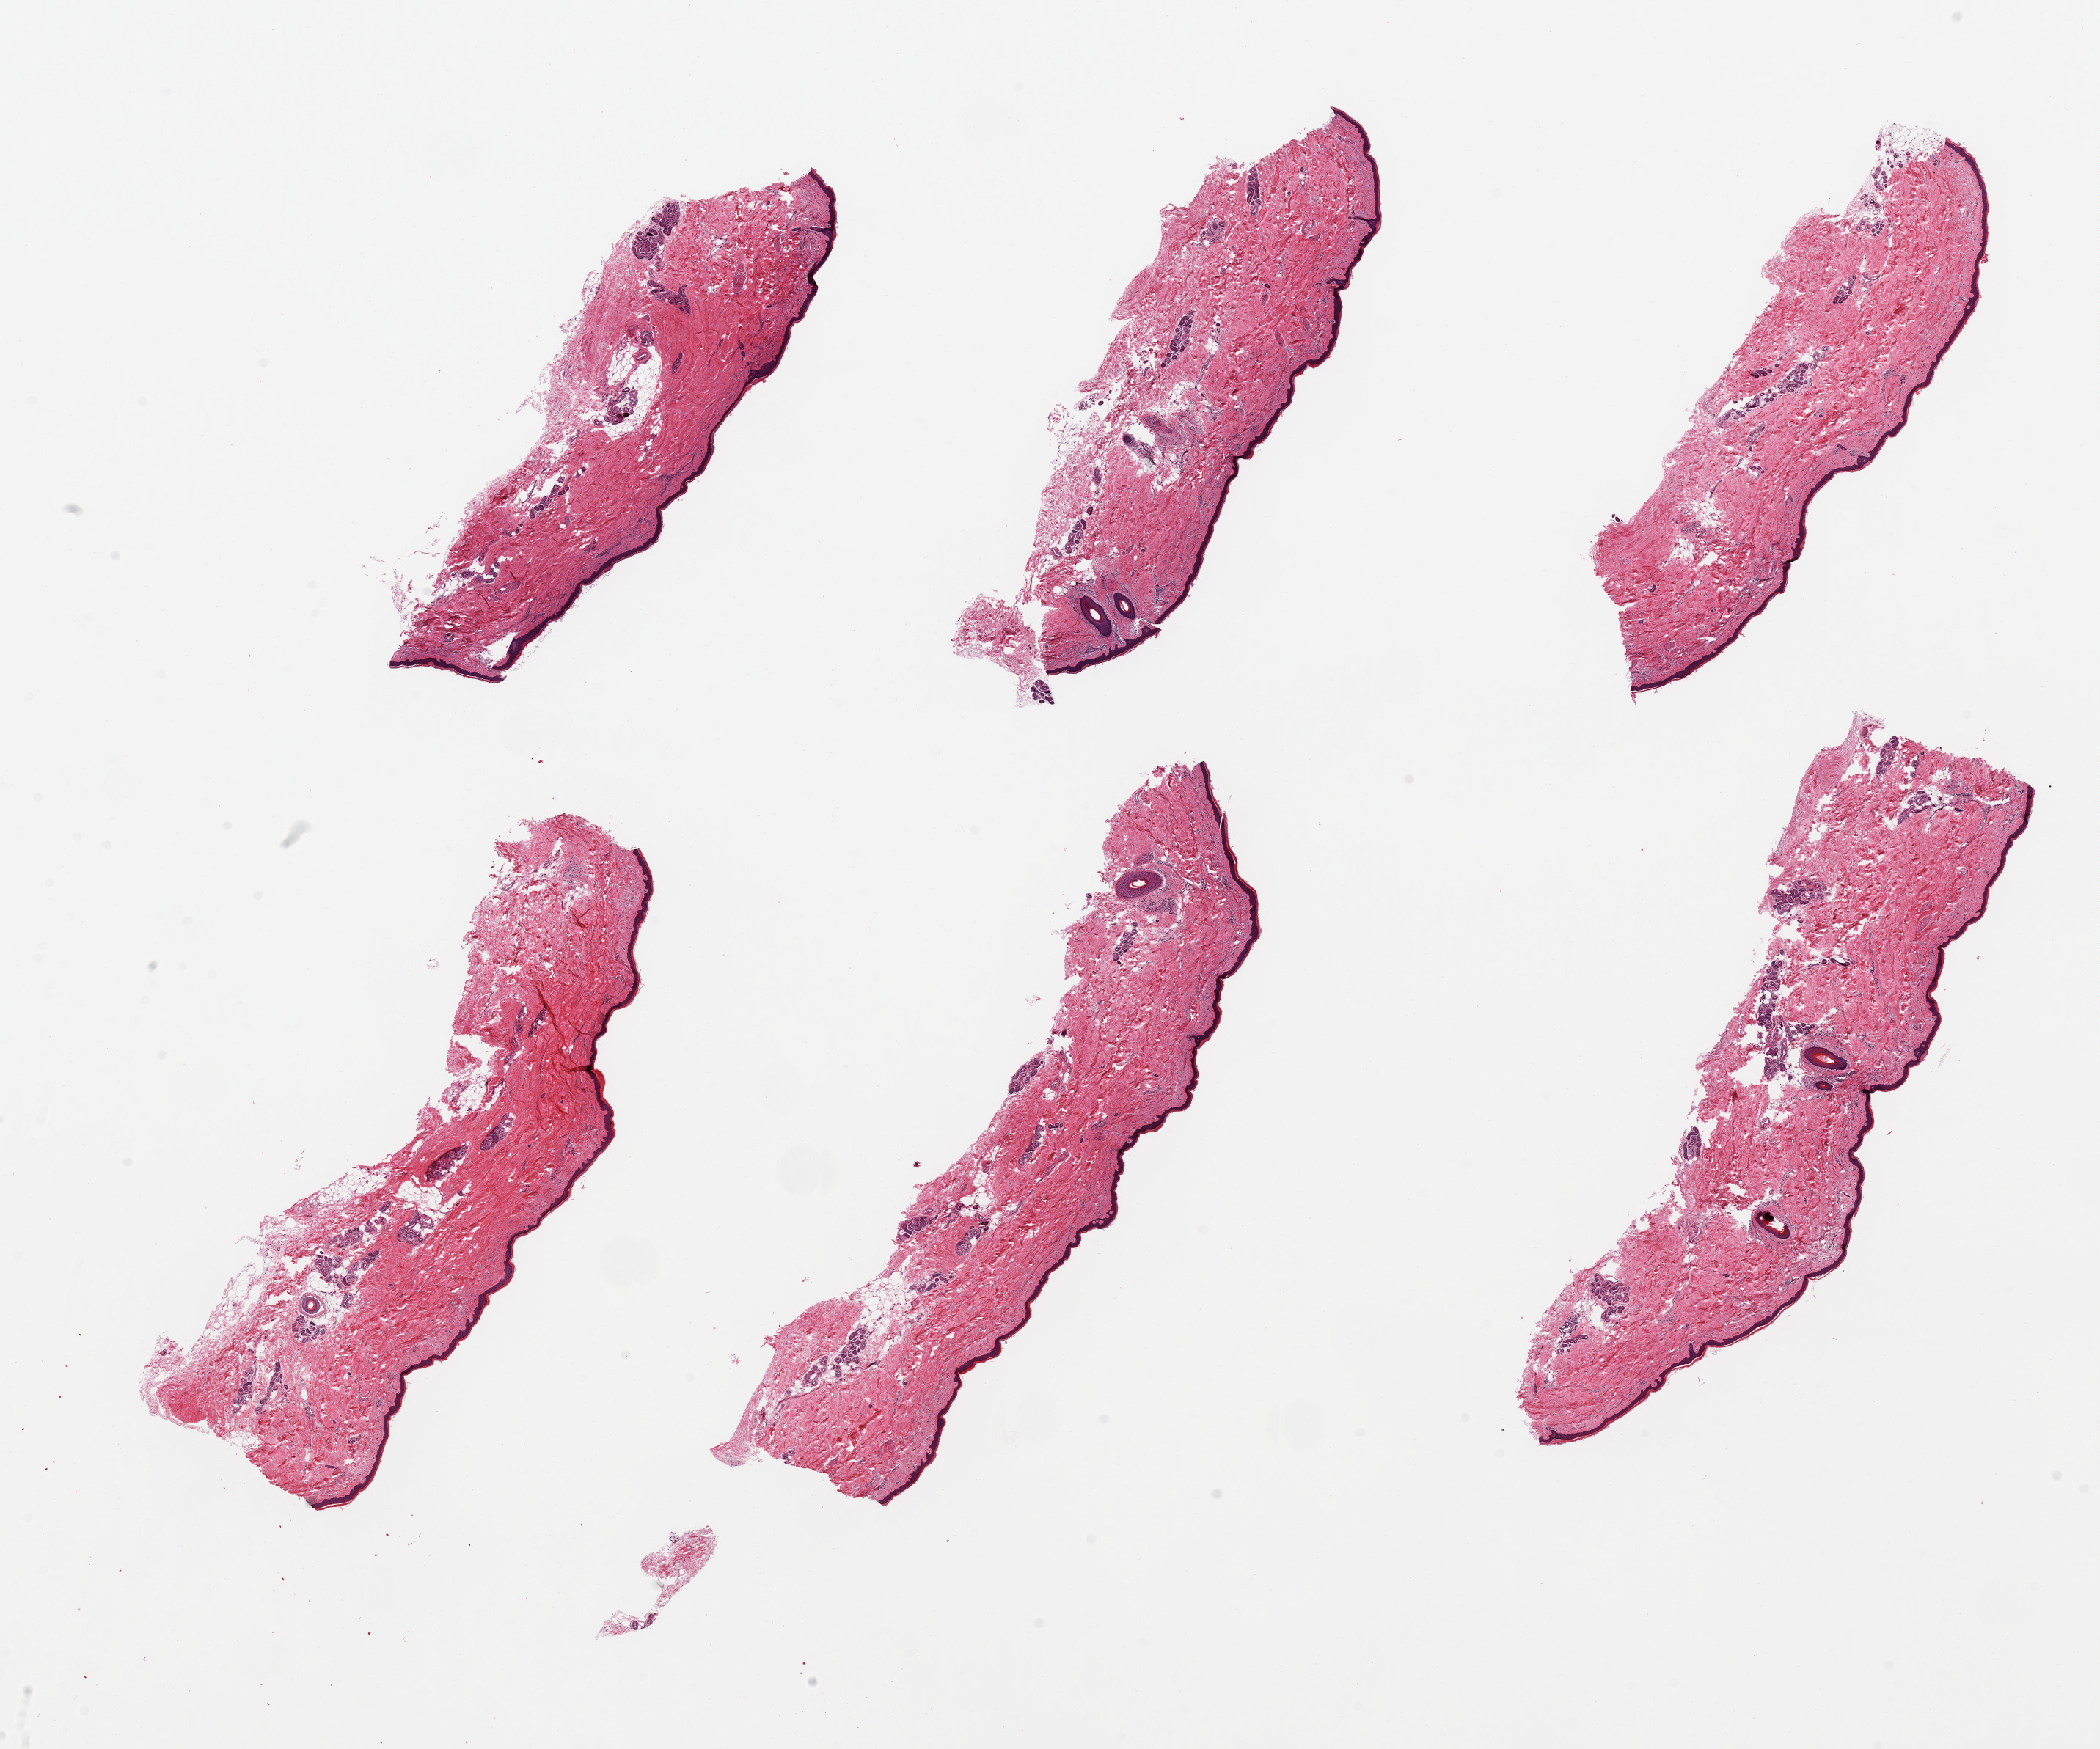
Digitized haematoxylin and eosin-stained section, whole scanned area (about 22.6 x 18.9 mm) shown as a low-resolution overview; PAXgene-fixed paraffin-embedded (PFPE) section; target tissue: skin of lower leg; donor tissue sample. Donor sex: male.
Pathologist's review note for this sample: 6 pieces, minimal adherent fat; squamous epithelium is ~50 microns.